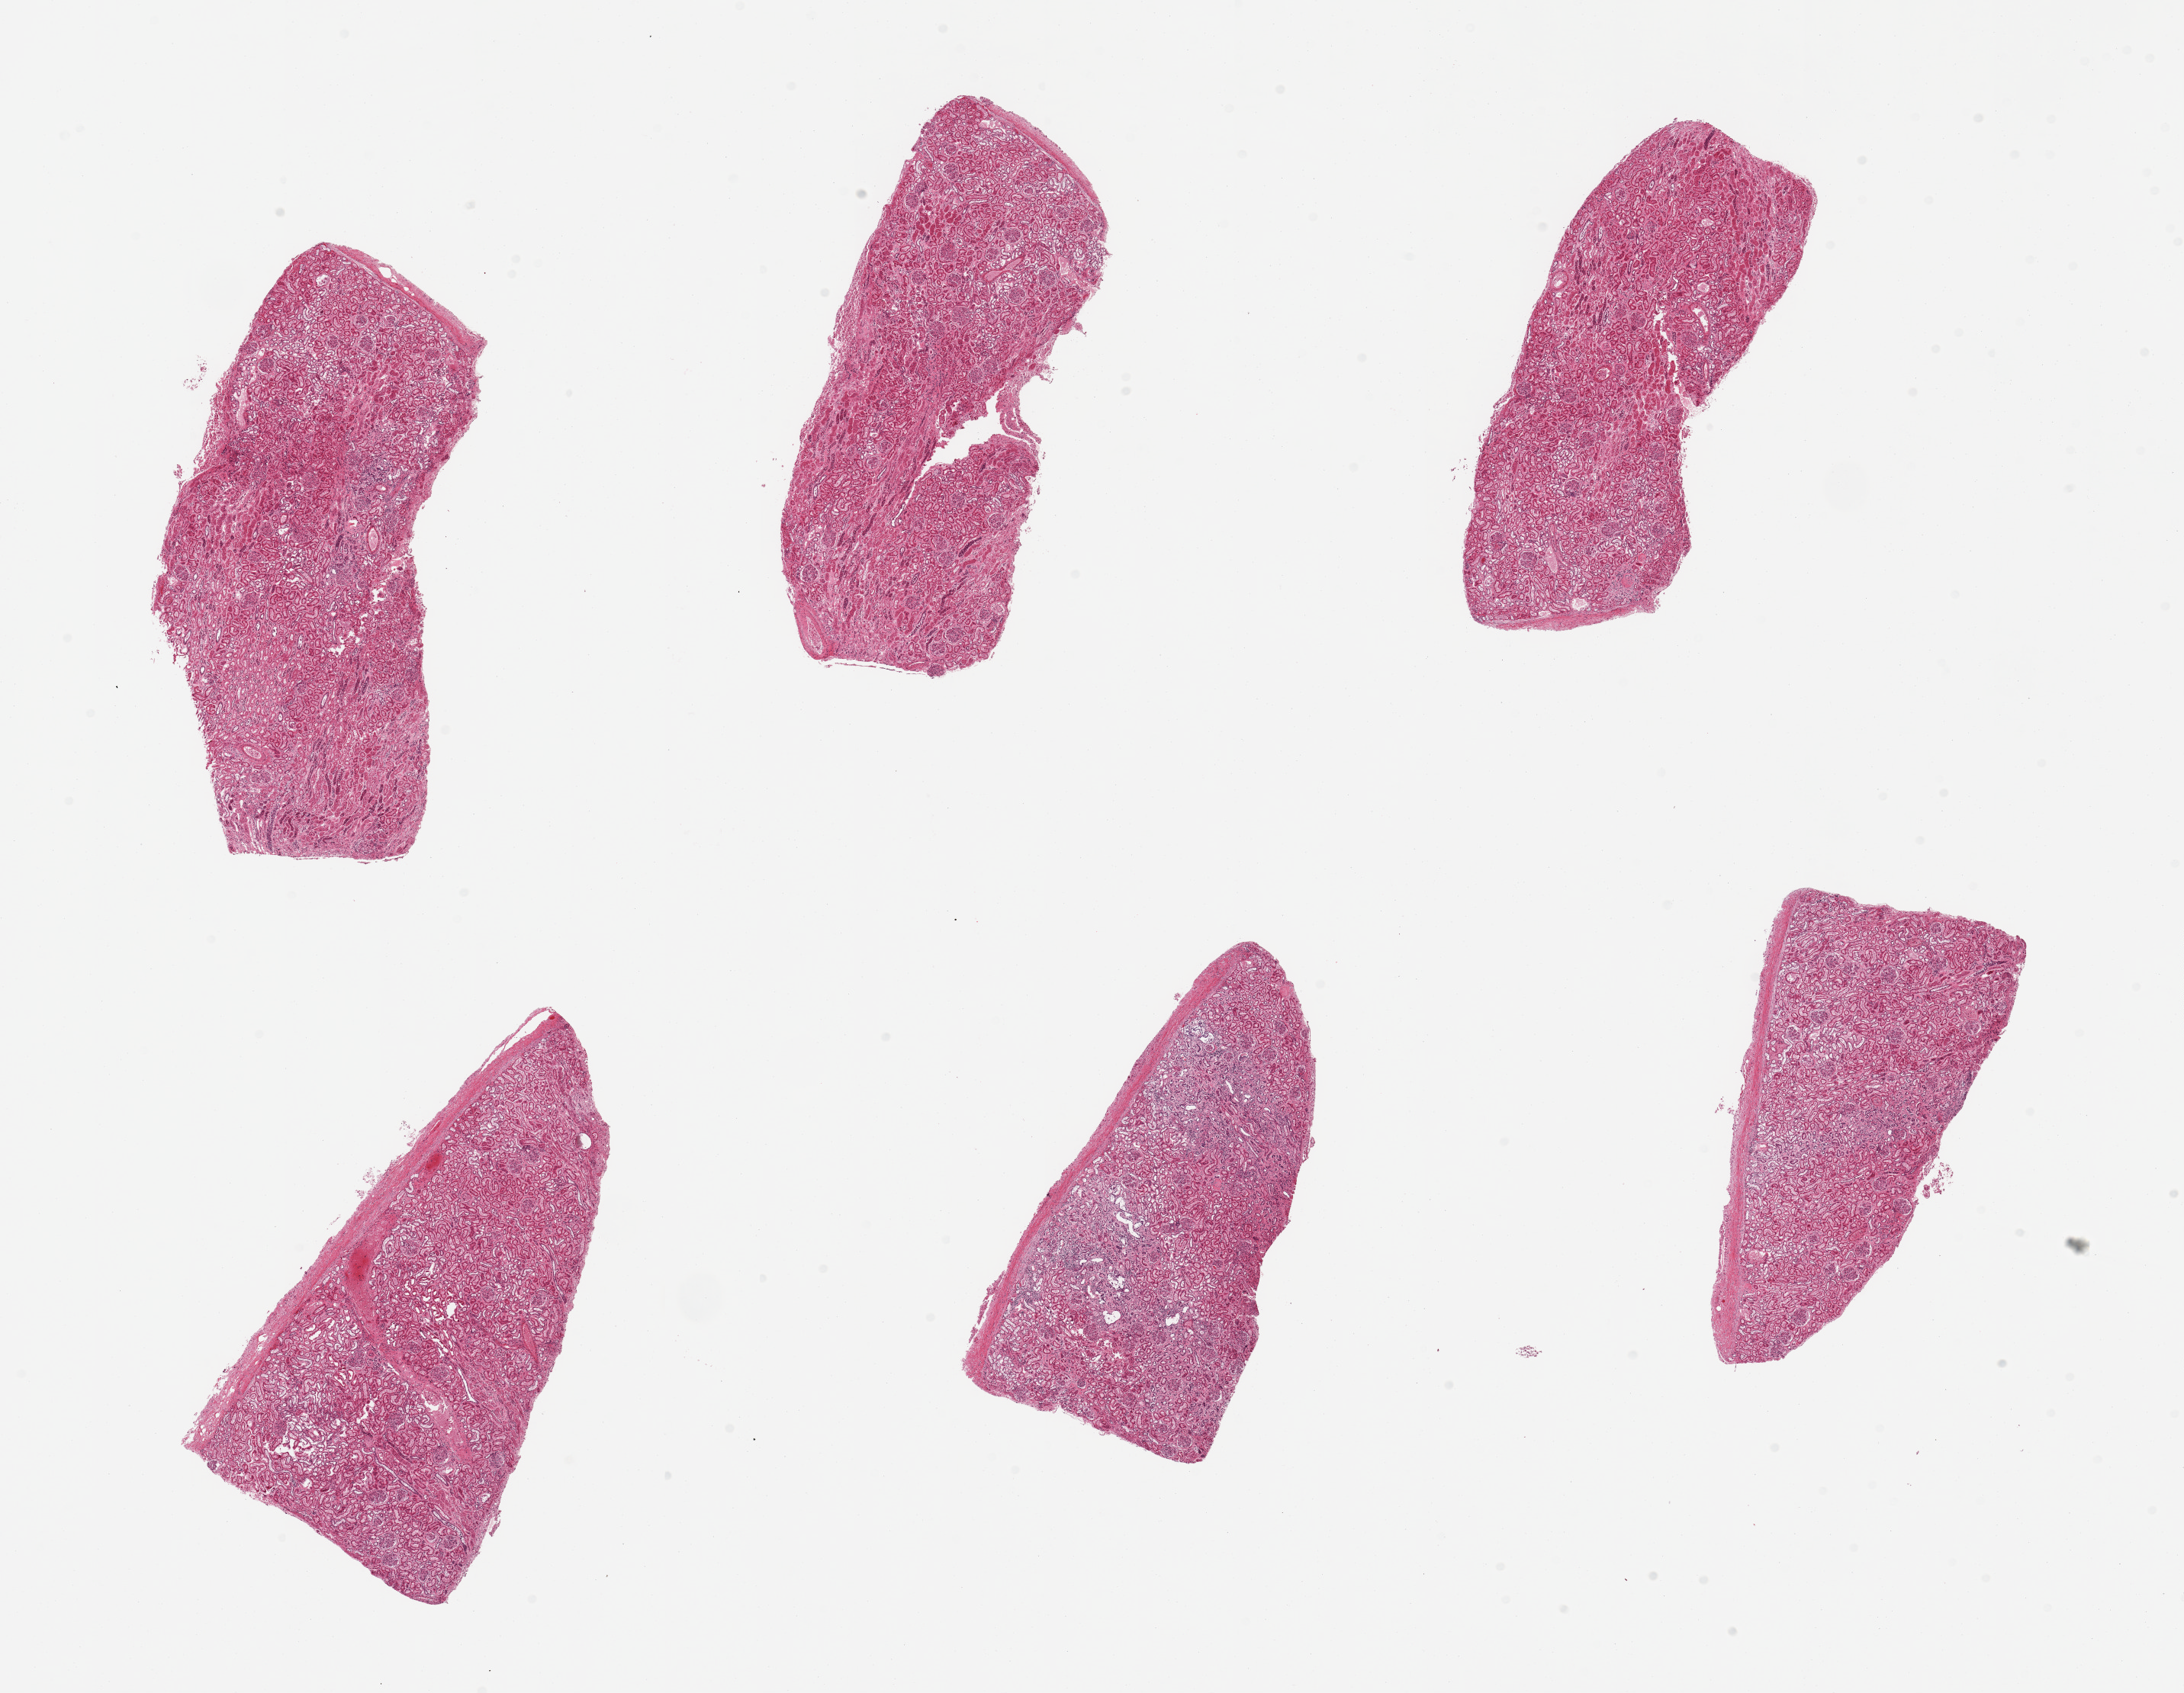
Digitized hematoxylin and eosin (H&E)-stained section — whole scanned area (about 22.6 x 17.6 mm, slide scanned at 20x) shown as a low-resolution overview, PAXgene-fixed, paraffin-embedded tissue, target tissue: renal cortex, tissue donor sample. Donor sex: female.
* review note (as recorded): 6 pieces, glomeruli present; better preserved than usual